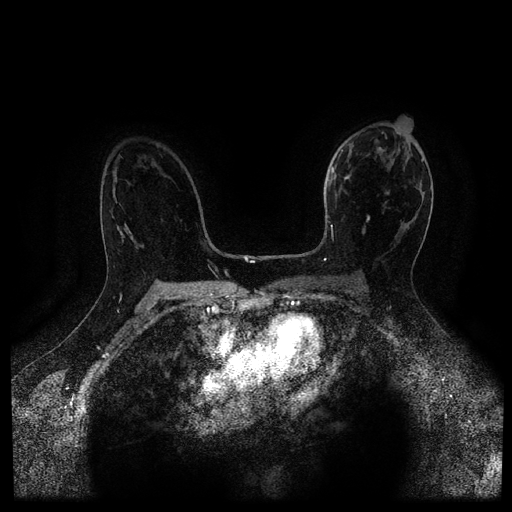
Breast MRI (dynamic contrast-enhanced, multi-phase), one axial slice. Dynamic contrast-enhanced series, time point 2 of 5 at this slice position (early post-contrast). 1.5 T. TE 2.7 ms, TR 5.4 ms. 2 mm slice thickness. 512 × 512 image matrix. Patient: female, 50 years.
Annotated regions visible in this slice (semi-automatically segmented with operator editing):
- breast lesion (labelled 'tumour' in the annotation; benign lesions carry a separate 'benign' label): bounding box <340,173,370,228> (left, top, right, bottom; pixels)